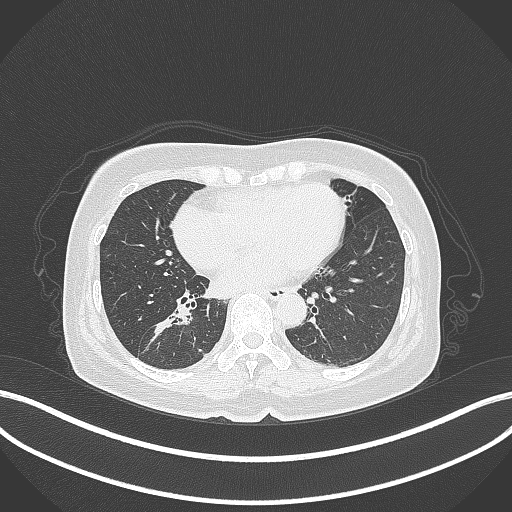
Chest CT, one axial slice. Position 159 of 429 along the scan axis. Reconstruction kernel B70f. Lung window (W 1500 / L -600 HU). 1 mm slice thickness. 512 × 512 image matrix, field of view 400 × 400 mm. Female patient, age 67 years. Case-level facts recorded for this patient, not image findings: clinical TNM (as recorded): T1c N1 M0; histopathological grade: G2-3.
Outlined on this slice (rectangle marked by the reading radiologist):
- lung tumour (recorded histology: adenocarcinoma): bounding box [x1, y1, x2, y2] px = [146, 307, 195, 354]